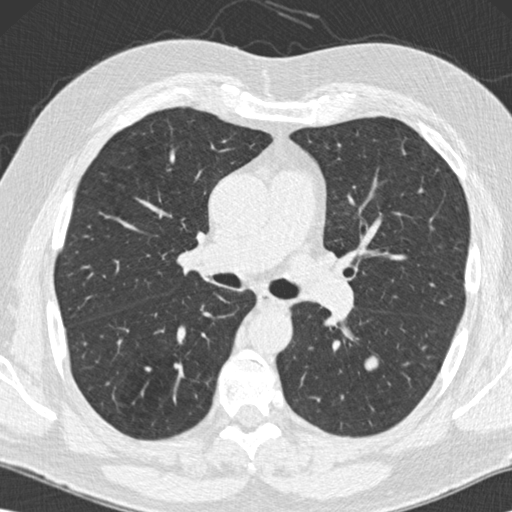
Low-dose screening chest CT, one axial slice. 120 kVp. Lung window (W 1500 / L -600 HU). 2 mm slice thickness. 512 × 512 image matrix.
Structures marked on this image (manually delineated by an expert):
- lesion 2 (nodule, lower lobe of left lung): box from (x=365, y=356) to (x=378, y=370) px